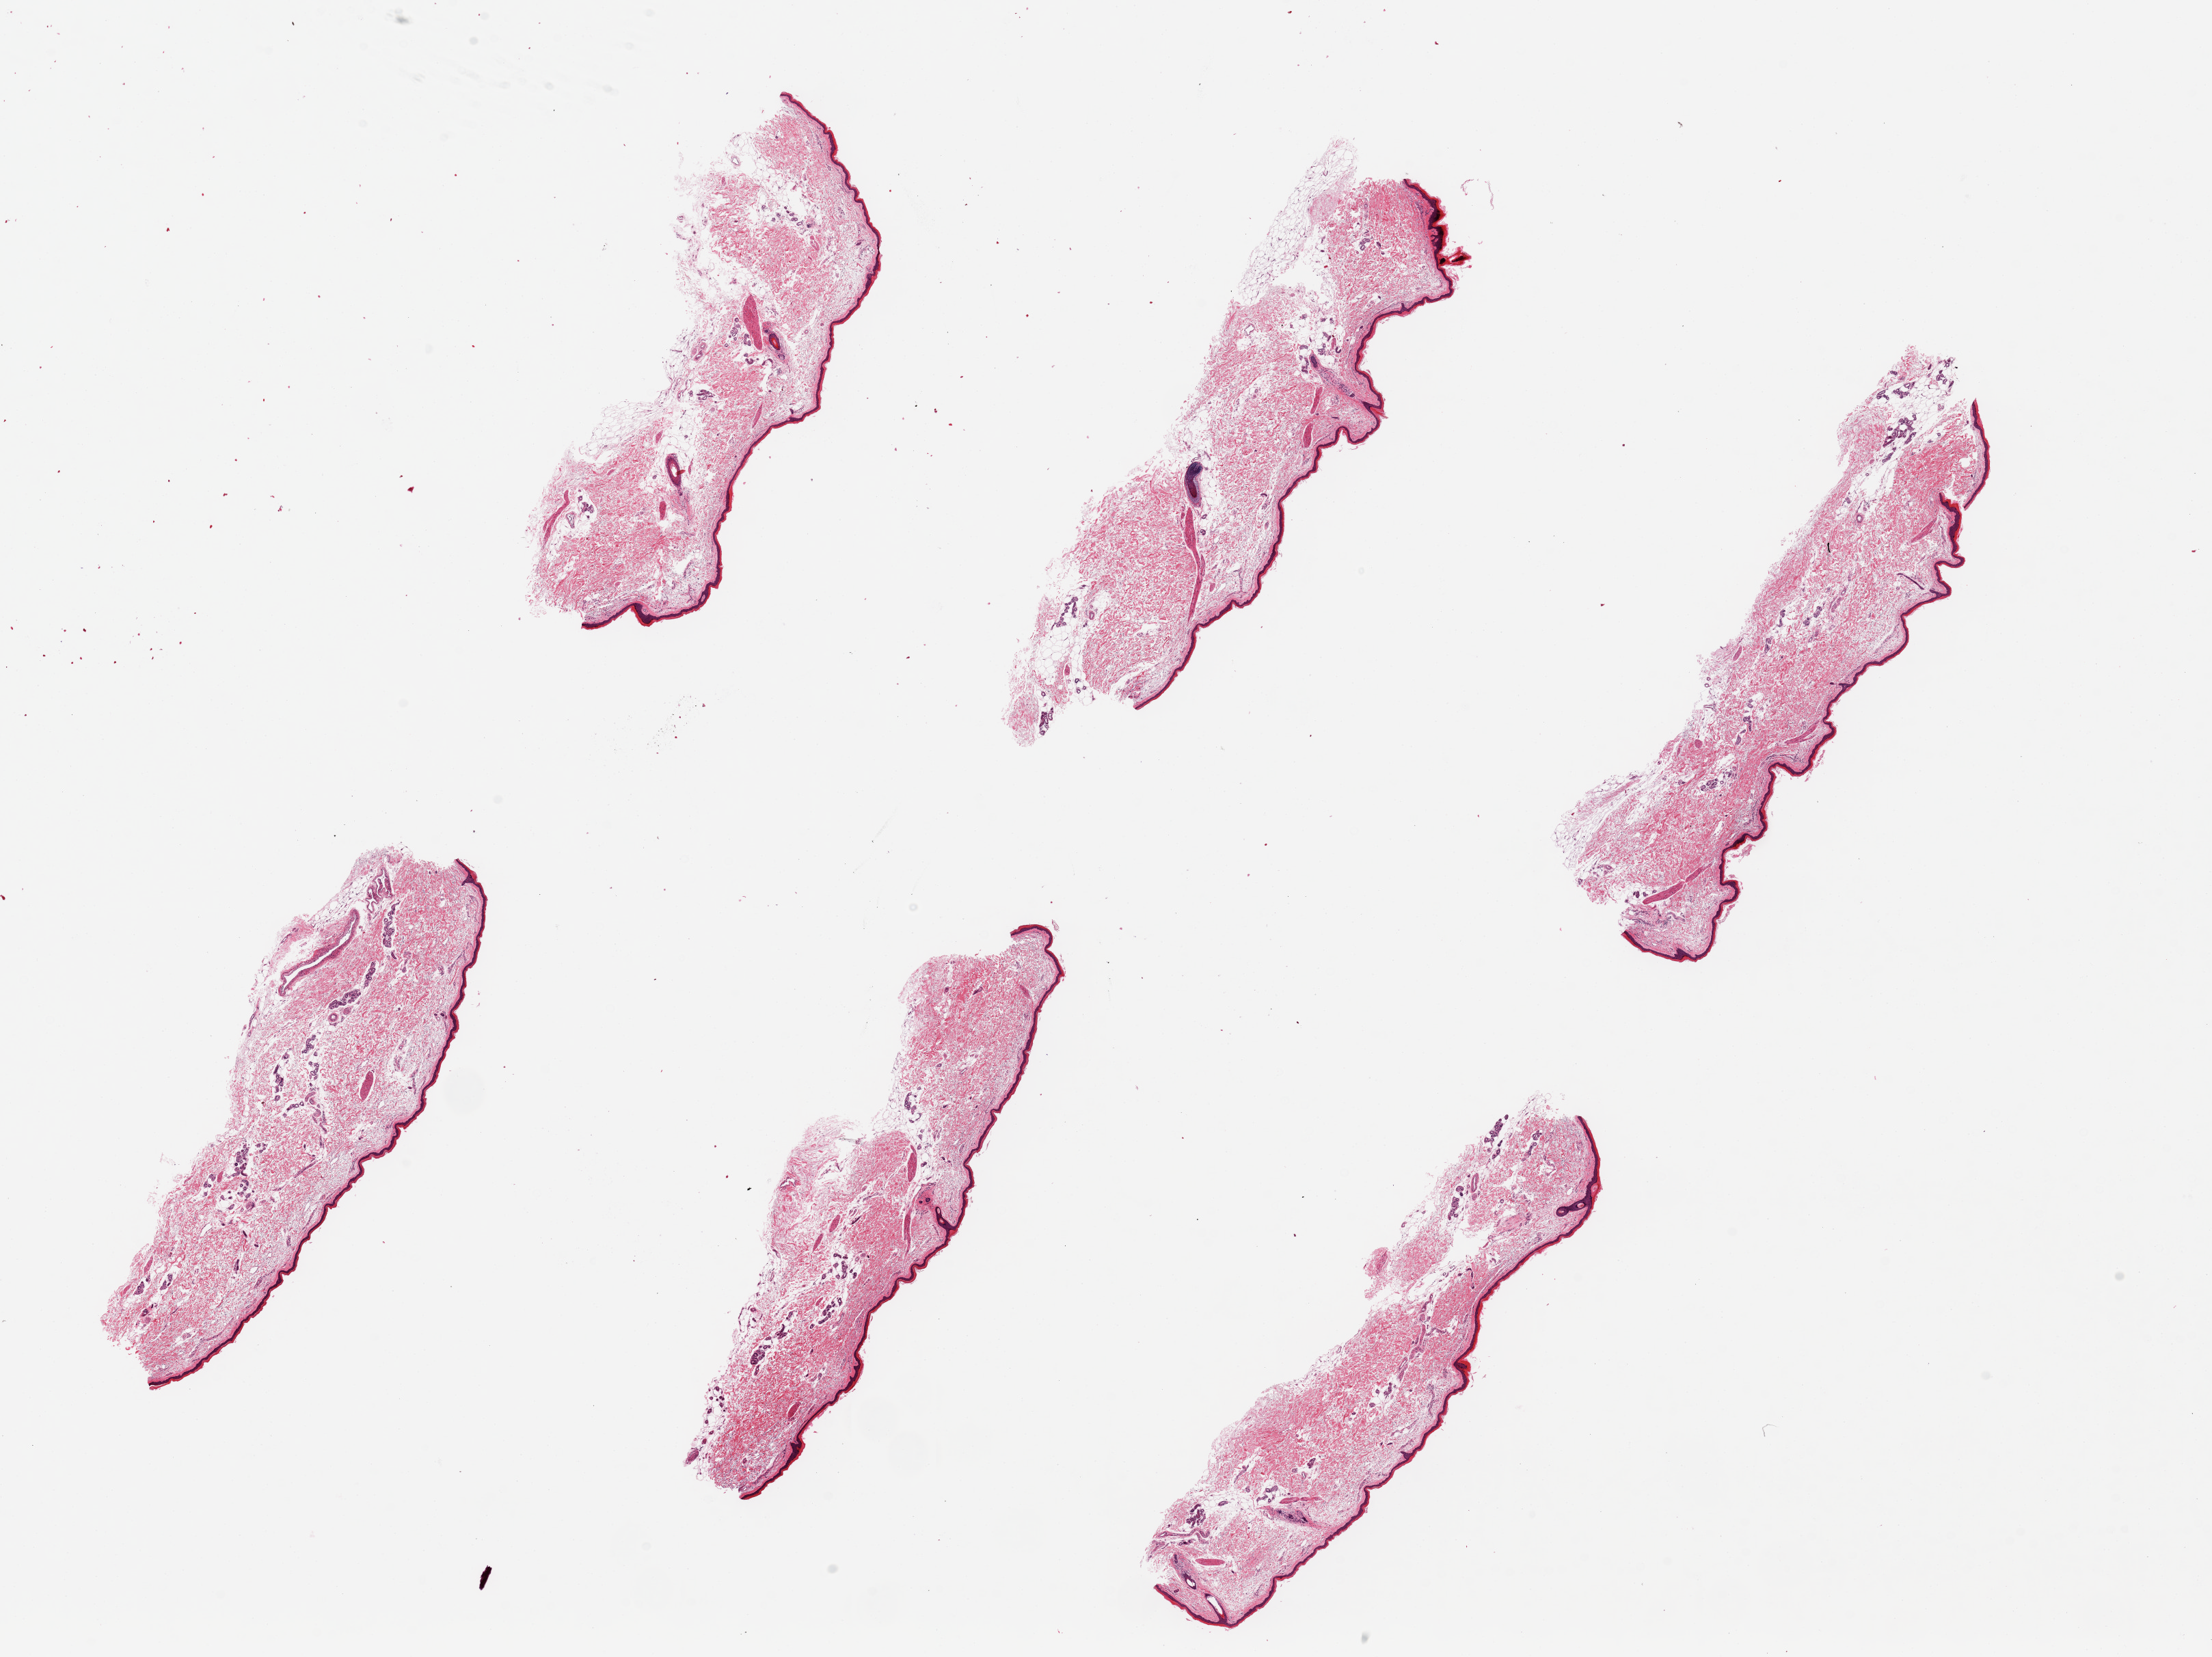
Haematoxylin and eosin whole-slide image — whole scanned area (about 25.6 x 19.2 mm) shown as a low-resolution overview, PAXgene-fixed paraffin-embedded (PFPE) section, section of skin of lower leg (target tissue), donor tissue sample. Donor sex: female.
• pathologist's review note for this sample: 6 pieces, up to 8x2mm; squamous epithelium peculiarly atrophic, less than 1% thickness